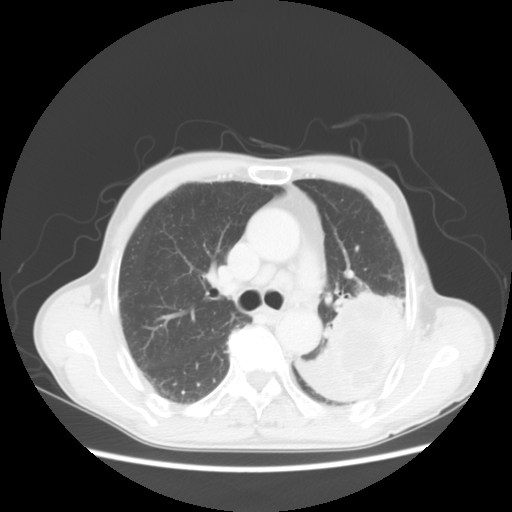
Chest CT, one axial slice. Position 34 of 51 along the scan axis. Reconstruction kernel STANDARD. Lung window (W 1500 / L -600 HU). 5 mm slice thickness. 512 × 512 image matrix. Male patient, age 64 years. Case-level facts recorded for this patient, not image findings: clinical TNM (as recorded): T4 N0 M0; histopathological grade: G2-3.
Outlined on this slice (rectangle marked by the reading radiologist):
- lung tumour (recorded histology: squamous cell carcinoma): bounding box (x1, y1, x2, y2) in pixels: (301, 275, 401, 406)